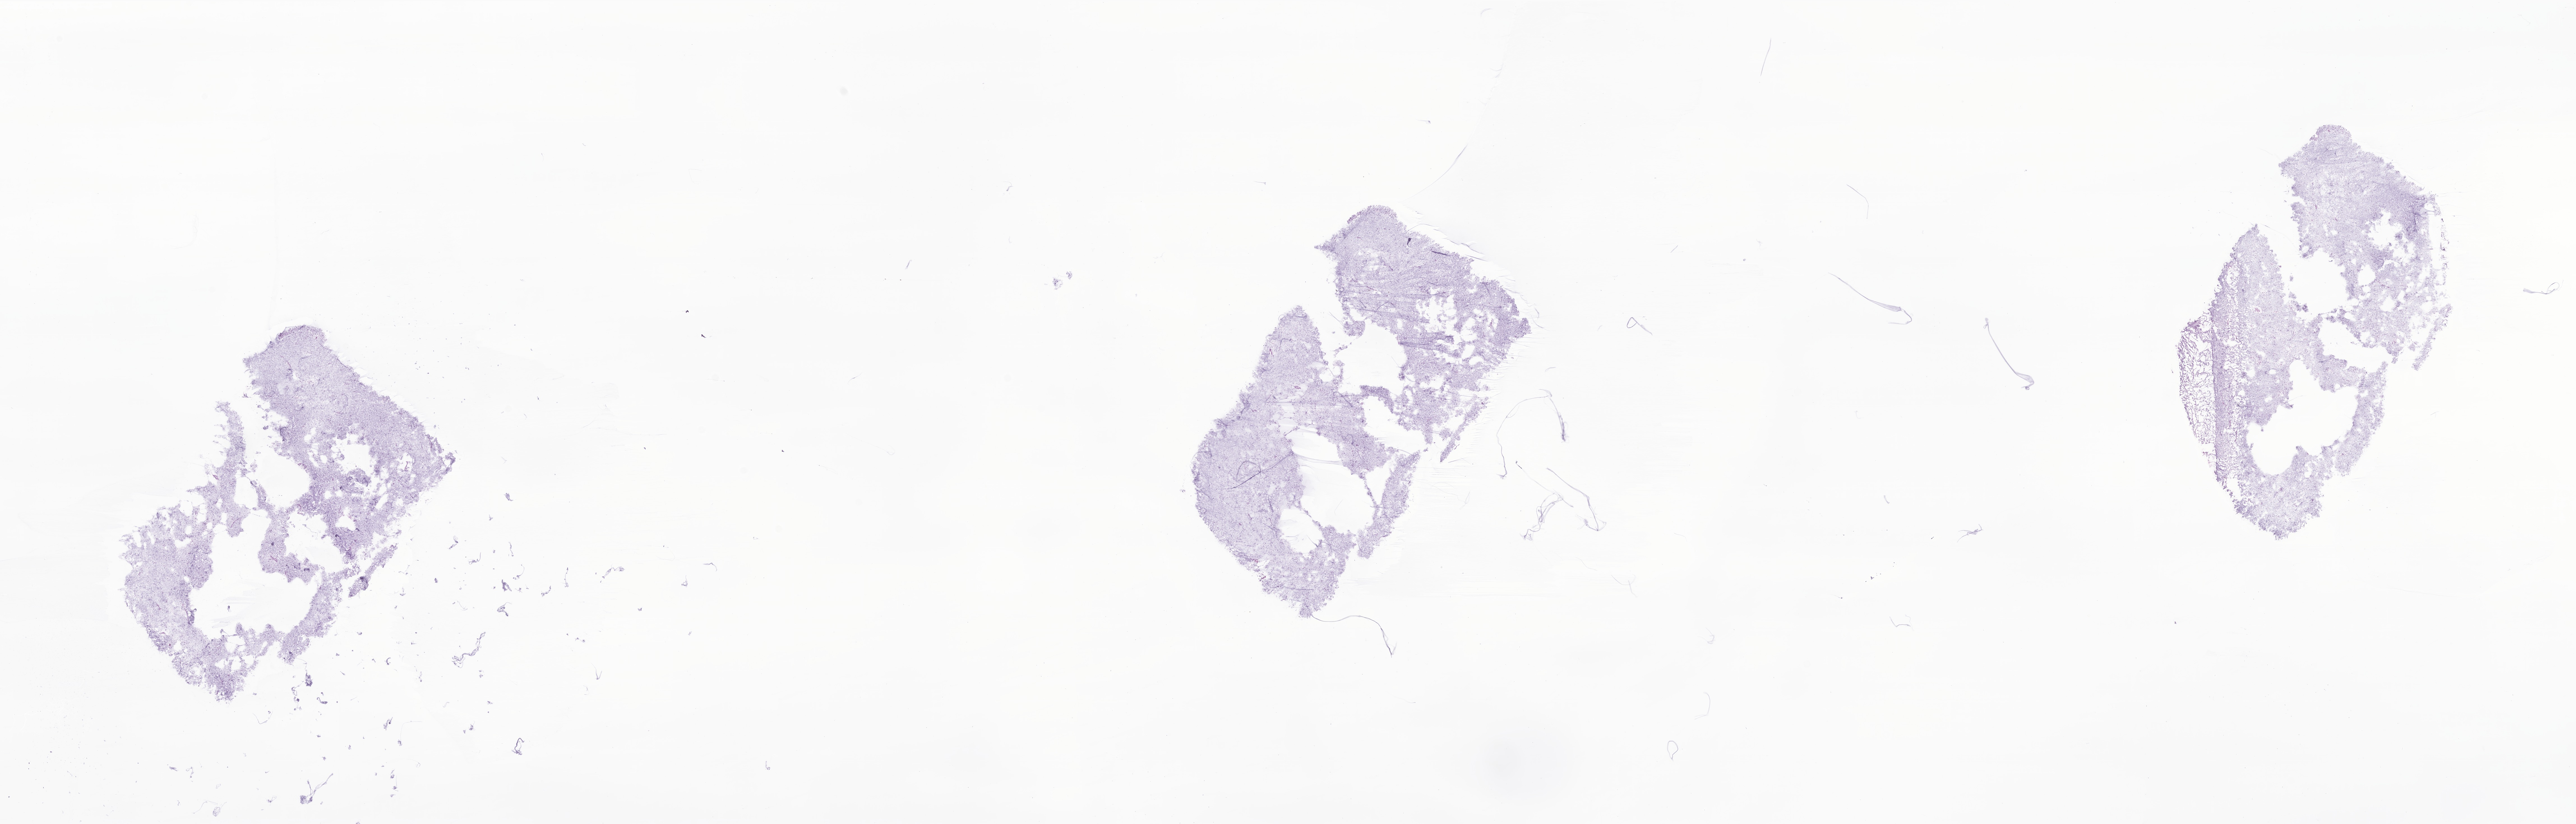
Whole-slide image, hematoxylin and eosin (H&E) stain of tumor tissue from the frontal lobe — whole scanned area (about 38.7 x 12.4 mm) shown as a low-resolution overview, frozen section. Patient: male, age 71 months (5 years 11 months).
* recorded diagnosis: Astrocytoma, NOS